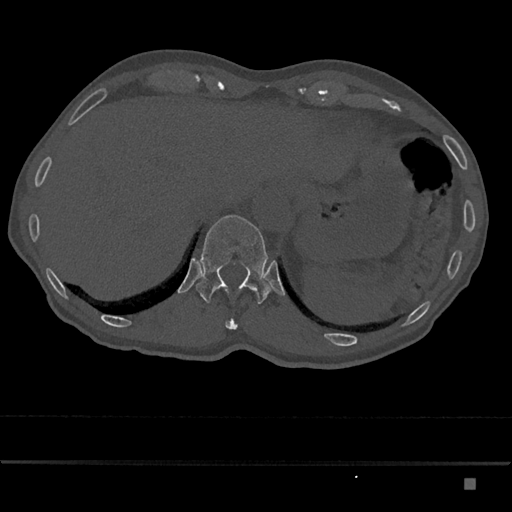
CT including the spine, one axial slice. Position 628 of 797 along the scan axis. Bone window (W 1800 / L 400 HU). 512 × 512 image matrix. Male patient, age 72 years. From the clinical record (not read from this slice): primary cancer: prostate.
Outlined on this slice (semi-automatic segmentation, software-assisted and operator-edited):
- T11 vertebra: bounding box [x1, y1, x2, y2] px = [225, 319, 238, 330]
- T12 vertebra: [196, 215, 271, 304]